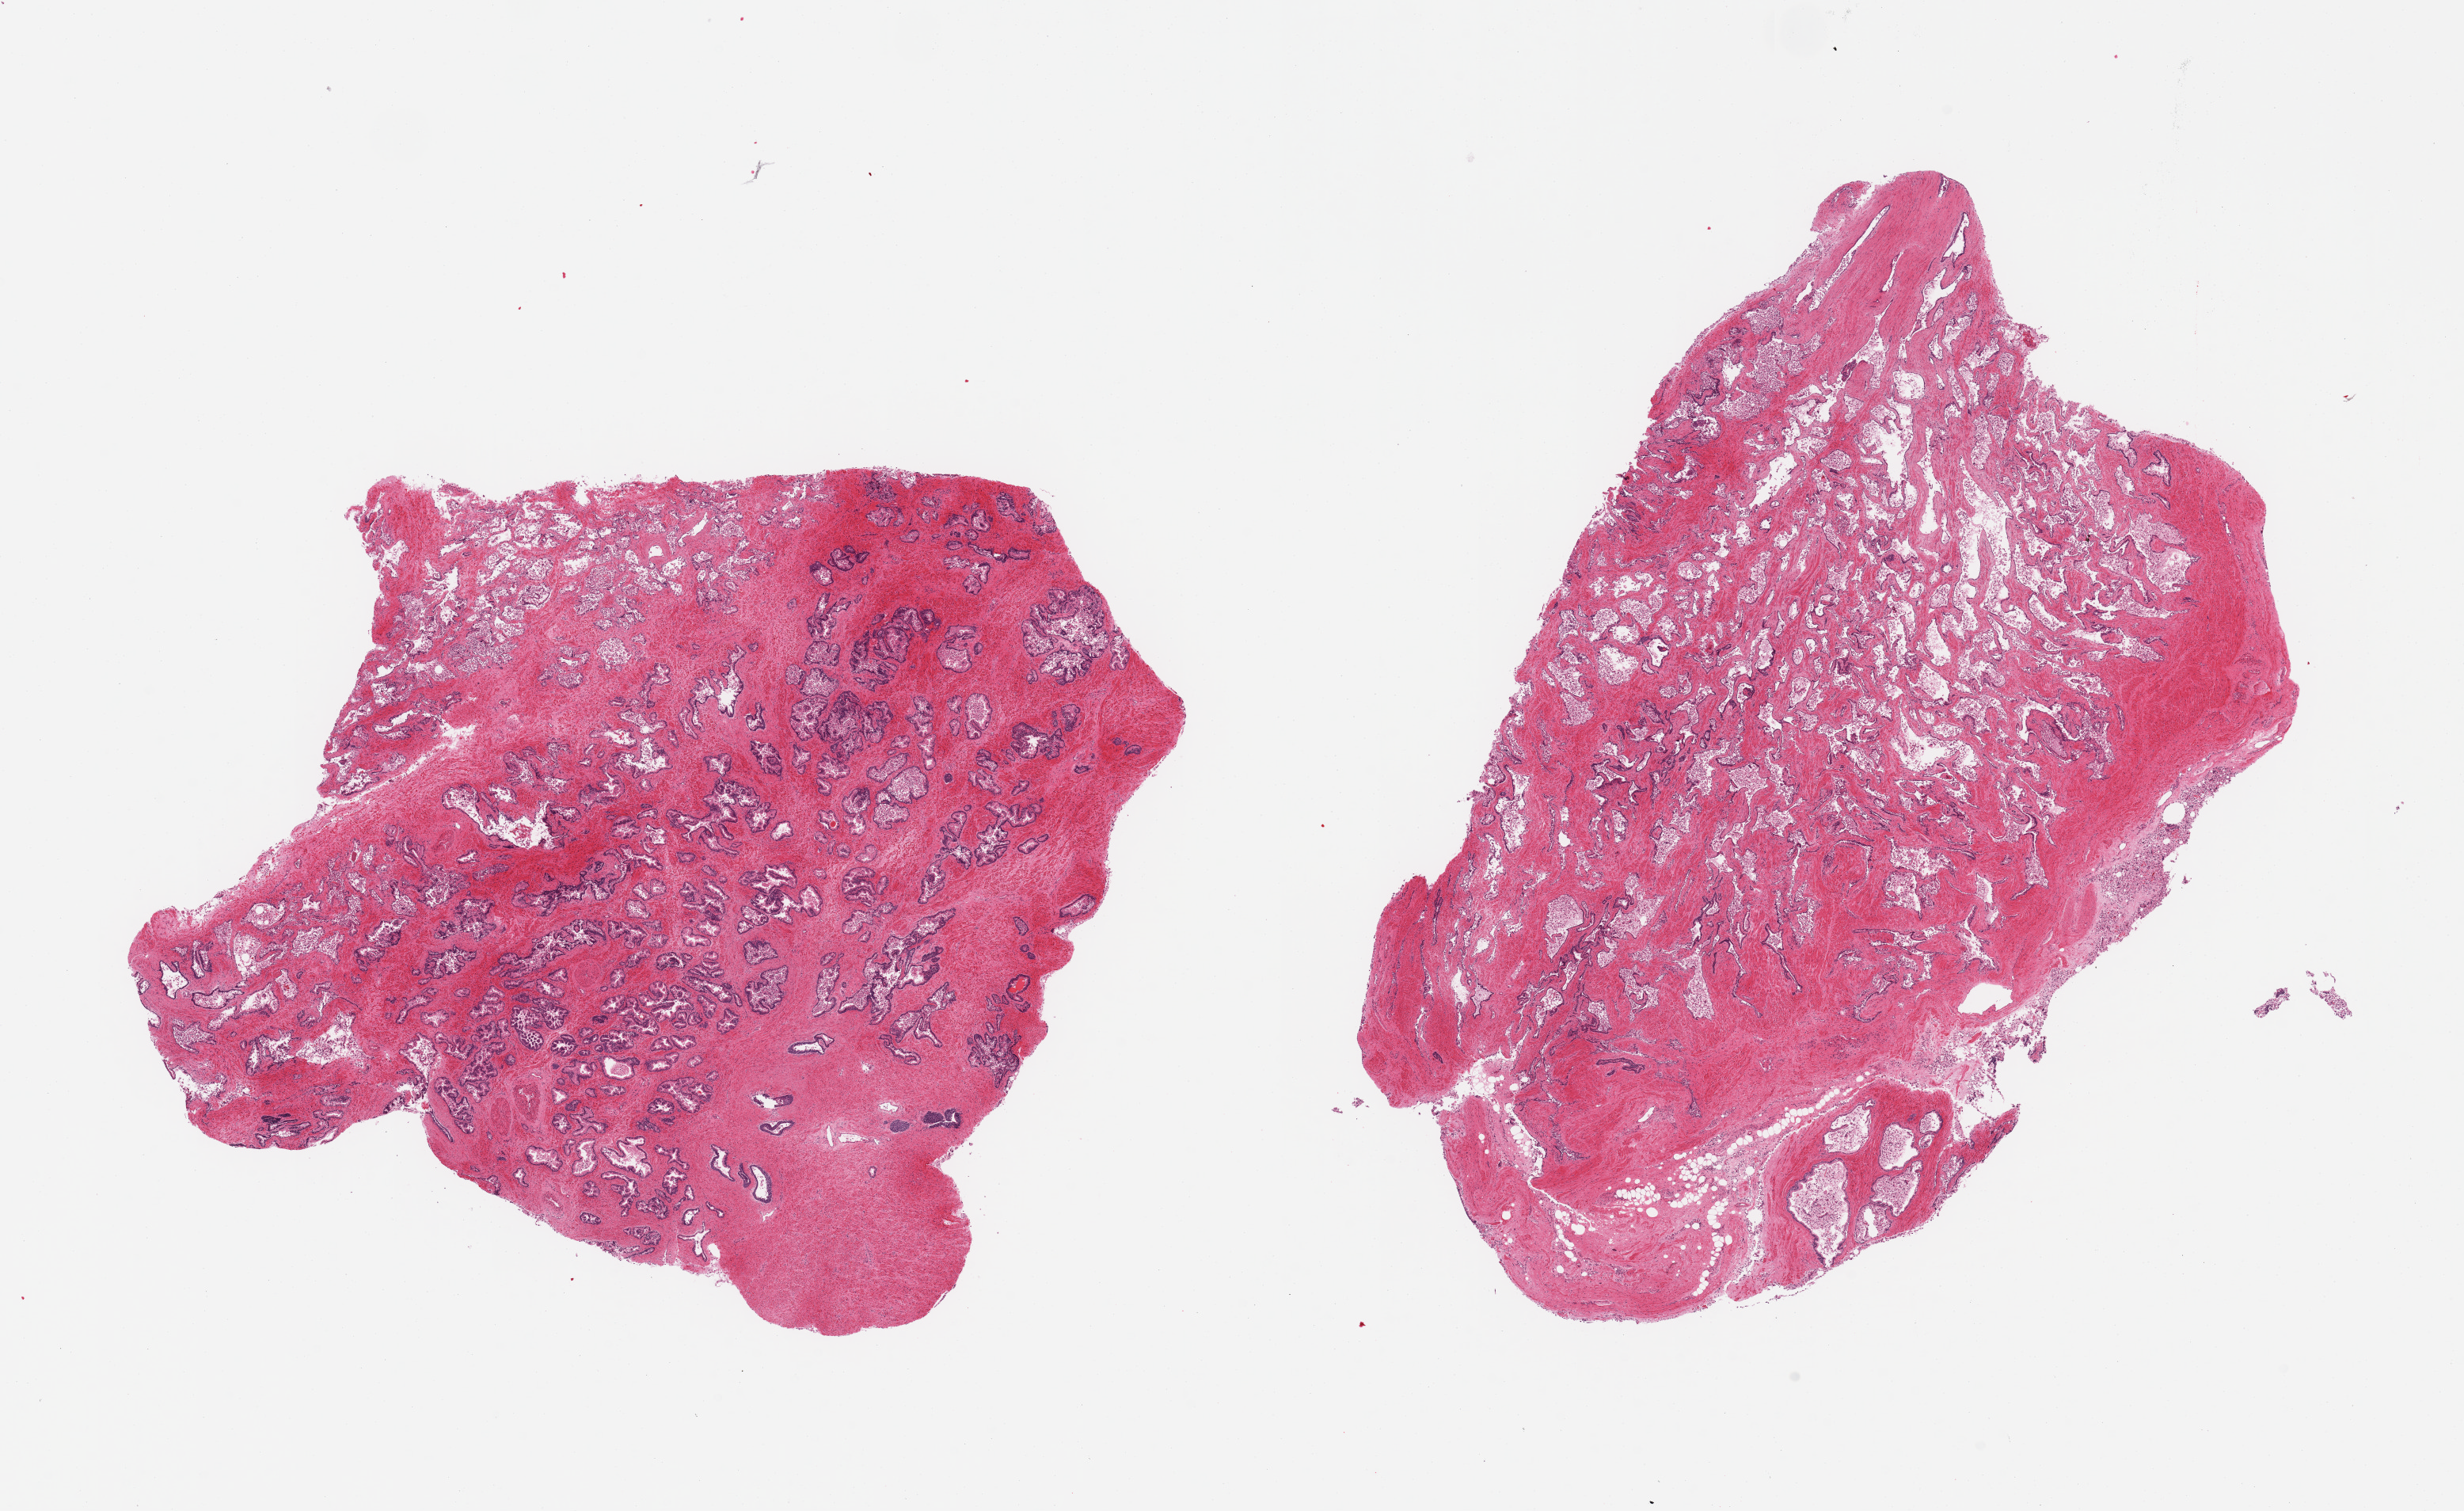
Haematoxylin and eosin whole-slide image, whole scanned area (about 24.6 x 15.1 mm) shown as a low-resolution overview; PAXgene-fixed, paraffin-embedded tissue; section of prostate (target tissue); donor tissue sample.
Reviewer comment on this tissue sample: 2 pieces, hyperplastic glandular pattern; glandular epithelium with moderate-advanced autolysis.